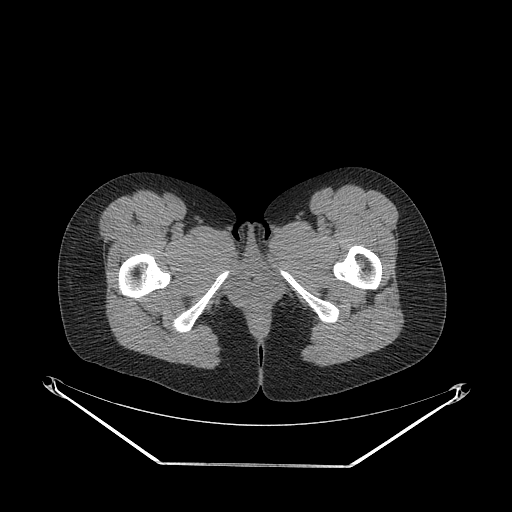
CT of an extremity soft-tissue mass (from a PET/CT study), one axial slice; position 50 of 267 along the scan axis; soft-tissue window (W 400 / L 40 HU); 3.75 mm slice thickness; 512 × 512 image matrix, field of view 500 × 500 mm. Female patient. From the clinical record (not read from this slice): histological type: synovial sarcoma; grade: intermediate; site of the primary tumour: right thigh.
Outlined on this slice (expert contour drawn on MRI and transferred to this co-registered scan by the dataset authors):
- gross tumour volume including surrounding oedema: bounding box (x1, y1, x2, y2) in pixels: (96, 222, 111, 241)
- gross tumour volume (mass): (94, 222, 111, 241)